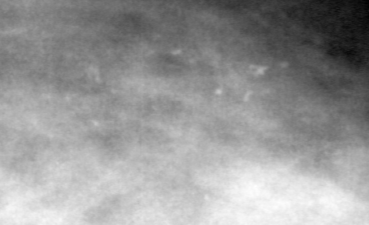
Cropped region of a digitized screen-film mammogram centred on a radiologist-marked abnormality; right breast; MLO view; BI-RADS breast density category 3 (scale 1–4).
Marked abnormality: calcifications, morphology pleomorphic, distribution clustered; BI-RADS assessment category 4; pathology result (as recorded, not read from the image): benign.